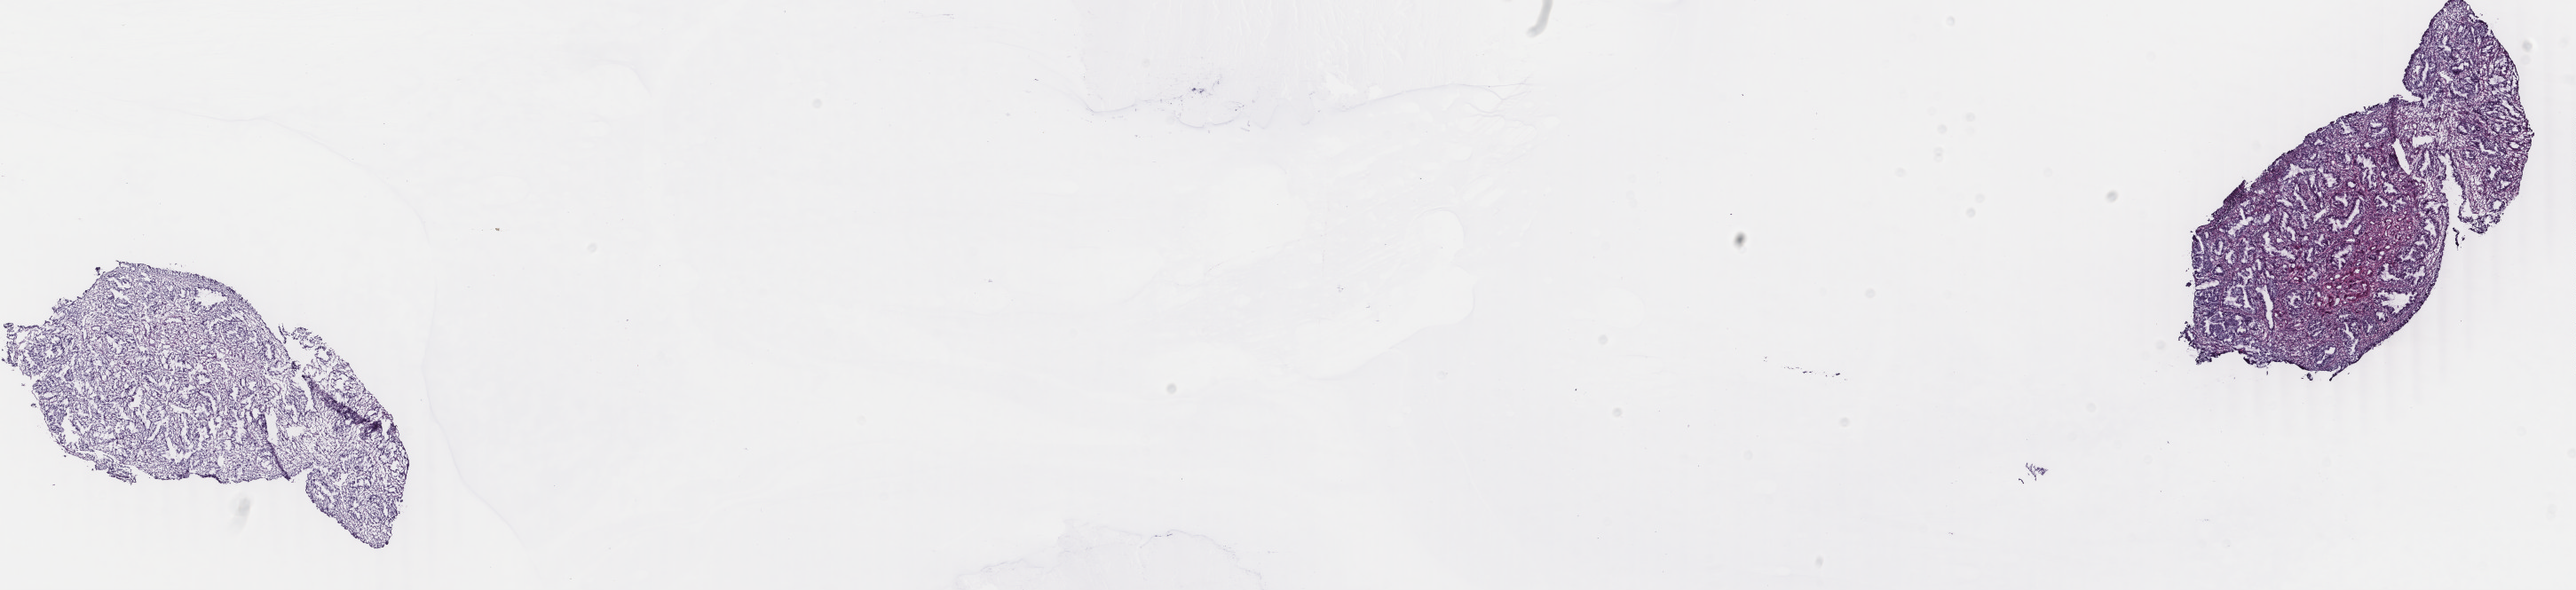
Whole-slide histology image, H&E — a low-resolution overview of the entire scanned area, about 23.1 x 5.3 mm; frozen section from the top of the tissue portion; primary tumour sample from the uterus. Patient: female, age at initial diagnosis 43 years. Histologic grade: G1 (well differentiated). Pathologist review of this section (percent, as recorded): tumour cells 70%, tumour nuclei 70%, normal cells 0%, stromal cells 30%, necrosis 0%. Inflammatory infiltration, as recorded: lymphocyte infiltration 30%, monocyte infiltration 2%, neutrophil infiltration 0%.
Pathologic diagnosis: Endometrioid adenocarcinoma, NOS. FIGO stage: IA.